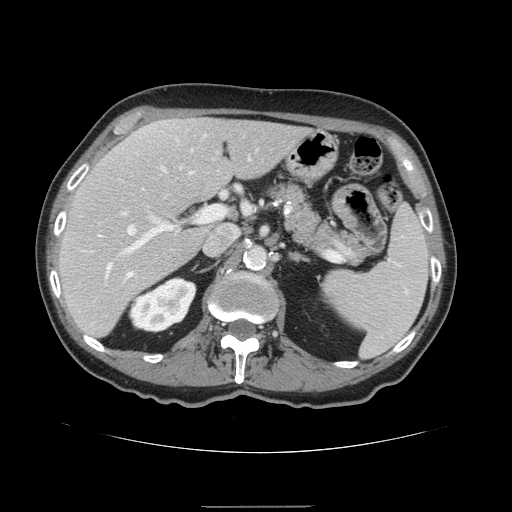
Contrast-enhanced abdominal CT, one axial slice; 120 kVp; soft-tissue window (W 400 / L 40 HU); 2.5 mm slice thickness; 512 × 512 image matrix, field of view 386 × 386 mm. Male patient, age 74 years. Case-level facts recorded for this patient, not image findings: diagnosis: colorectal cancer liver metastases, imaged before liver resection; multiple liver metastases: no; largest metastasis: 14.5 cm; chemotherapy before resection: no.
Outlined on this slice (outlined manually by an expert reader):
- hepatic veins: bounding box (x1, y1, x2, y2) in pixels: (127, 168, 165, 275)
- liver: (59, 118, 311, 338)
- planned liver remnant (the part of the liver to remain after resection): (59, 119, 312, 338)
- portal vein (with intrahepatic branches): (80, 207, 224, 272)